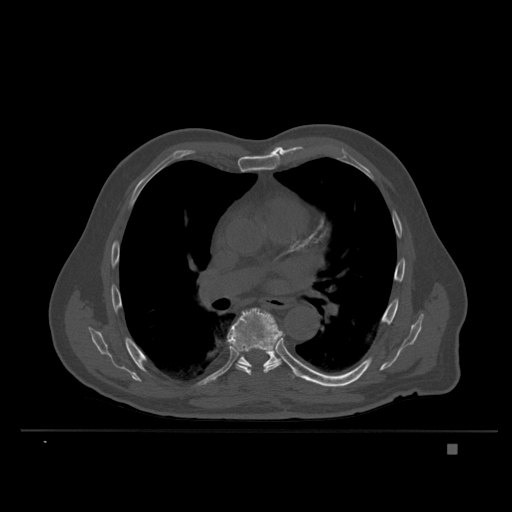
CT including the spine, one axial slice. Position 239 of 435 along the scan axis. Bone window (W 1800 / L 400 HU). 512 × 512 image matrix, field of view 434 × 434 mm. Male patient, age 73 years. Case-level facts recorded for this patient, not image findings: primary cancer: skin.
Structures marked on this image (semi-automatically segmented with operator editing):
- T7 vertebra: bounding box [x1, y1, x2, y2] px = [227, 308, 284, 376]
- T8 vertebra: [238, 352, 300, 379]